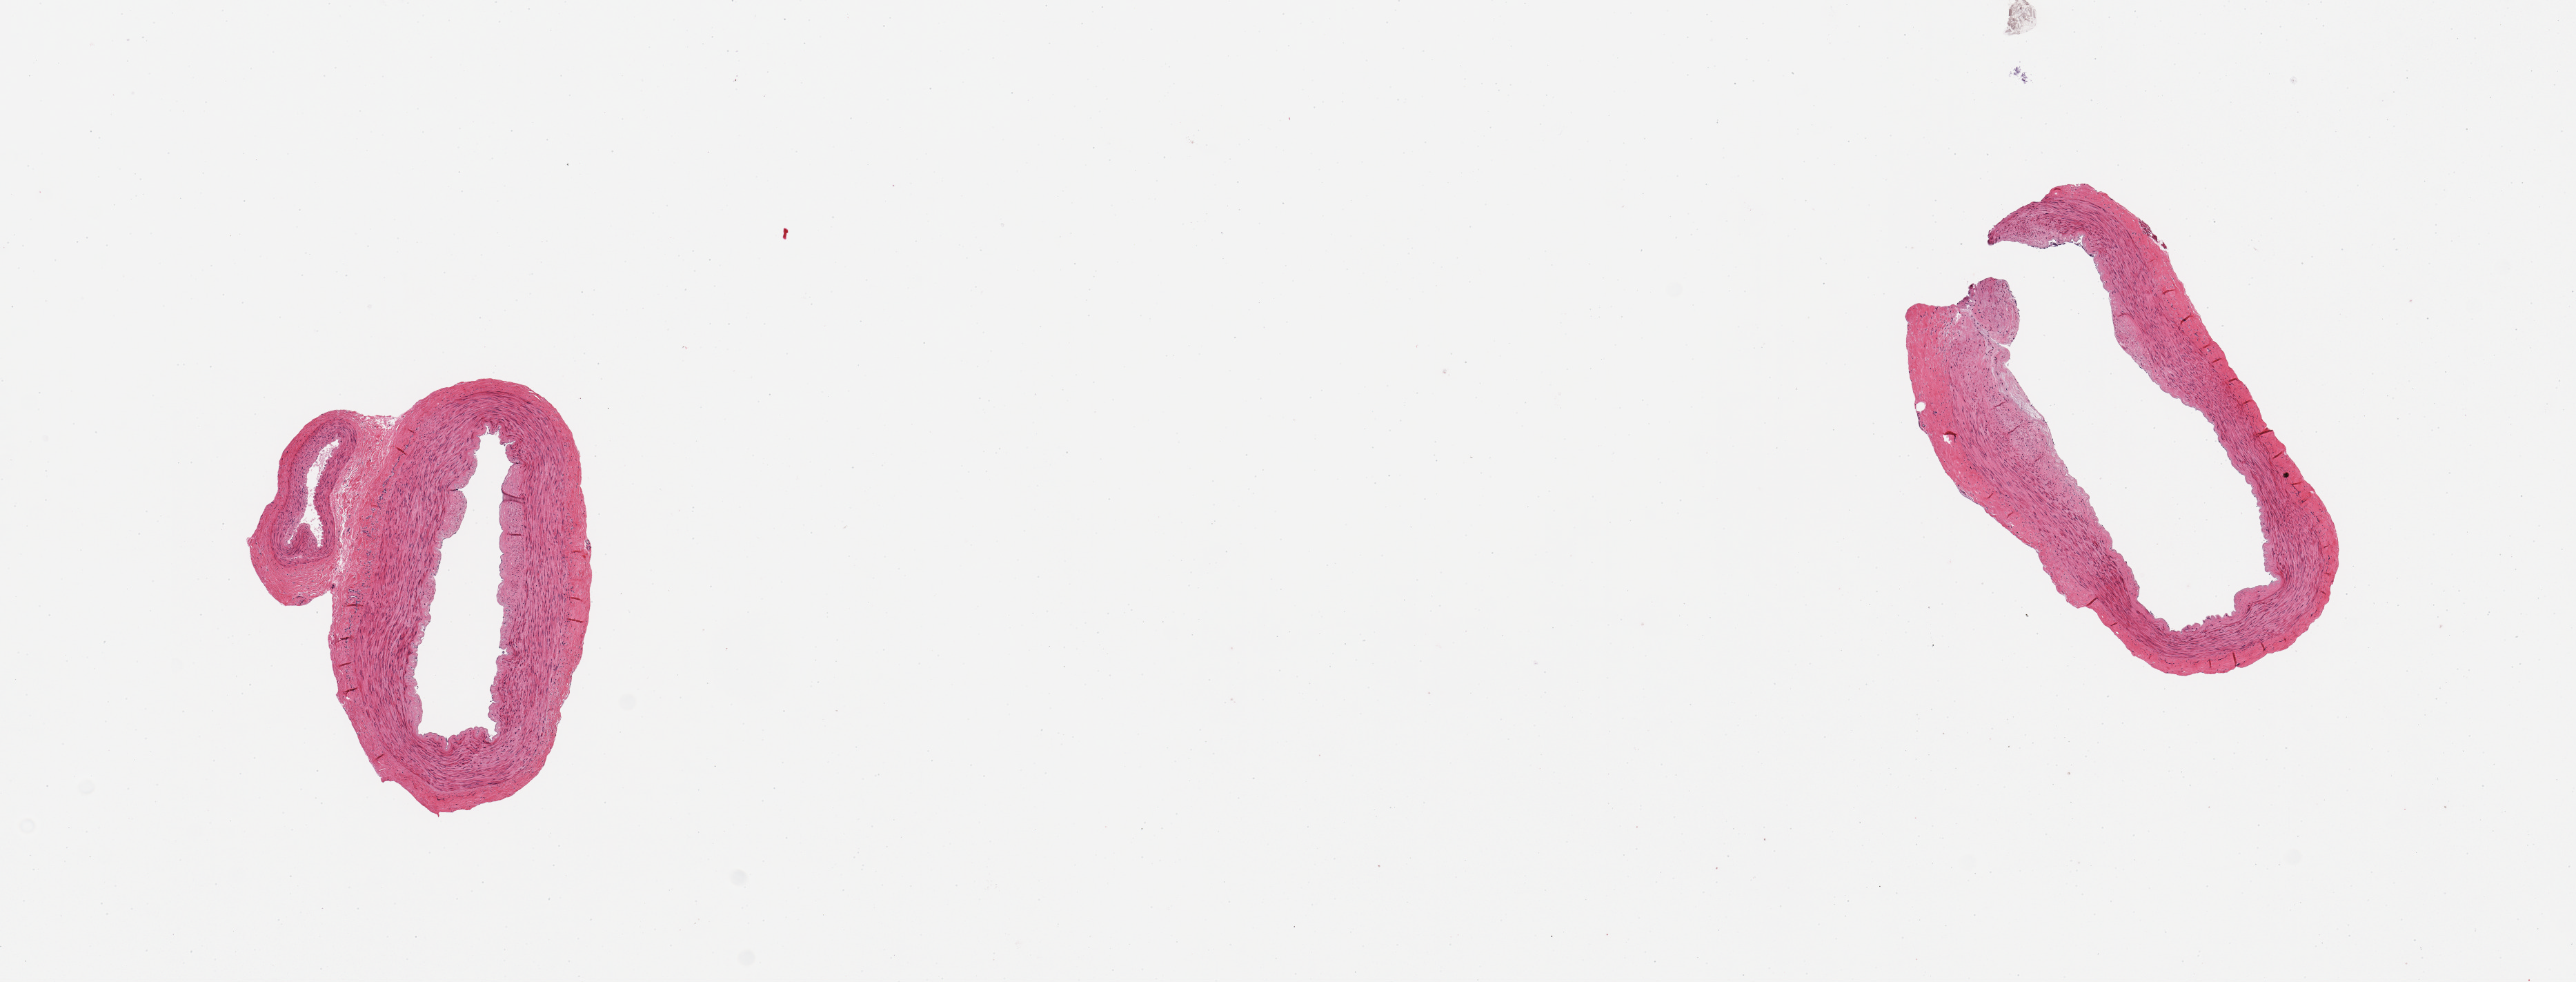
Haematoxylin and eosin whole-slide image, brightfield, a low-resolution overview of the entire scanned area, about 14.8 x 5.6 mm (from a 20x scan). PAXgene-fixed, paraffin-embedded tissue. Section of tibial artery (target tissue). Tissue donor sample. Donor sex: male.
Pathologist's review note for this sample: 2 pieces, no adherent fat, no atherosis.